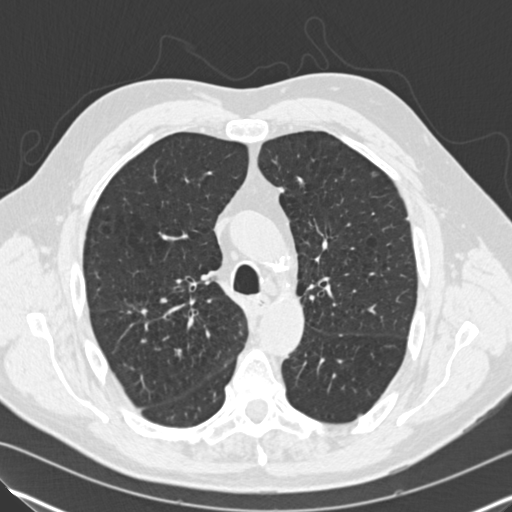
Chest CT (low-dose screening protocol), one axial image; first (baseline) screen; lung window (W 1500 / L -600 HU); 2 mm slice thickness; standard (soft-tissue) reconstruction kernel (B30f); slice 55 of 182 in the series; 512 × 512 image matrix. Male participant, aged 65 years at enrolment. Former smoker at enrolment.
- Expert reader's lesion annotation, bounding box (x1, y1, x2, y2) in pixels: (155, 337, 197, 375).
- The screening reader recorded 5 non-calcified nodules or masses ≥4 mm on this exam; which of them this box marks is not recorded.
- Official screen result: positive, change unspecified: nodule(s) >= 4 mm or enlarging nodule(s), mass(es), or other non-specific abnormalities suspicious for lung cancer.
- Later outcome: lung cancer diagnosed 814 days after this screen (after the third annual screen) — adenocarcinoma, NOS, right upper lobe, moderately differentiated (G2), stage IA (AJCC 6th edition), 16 mm at pathology.